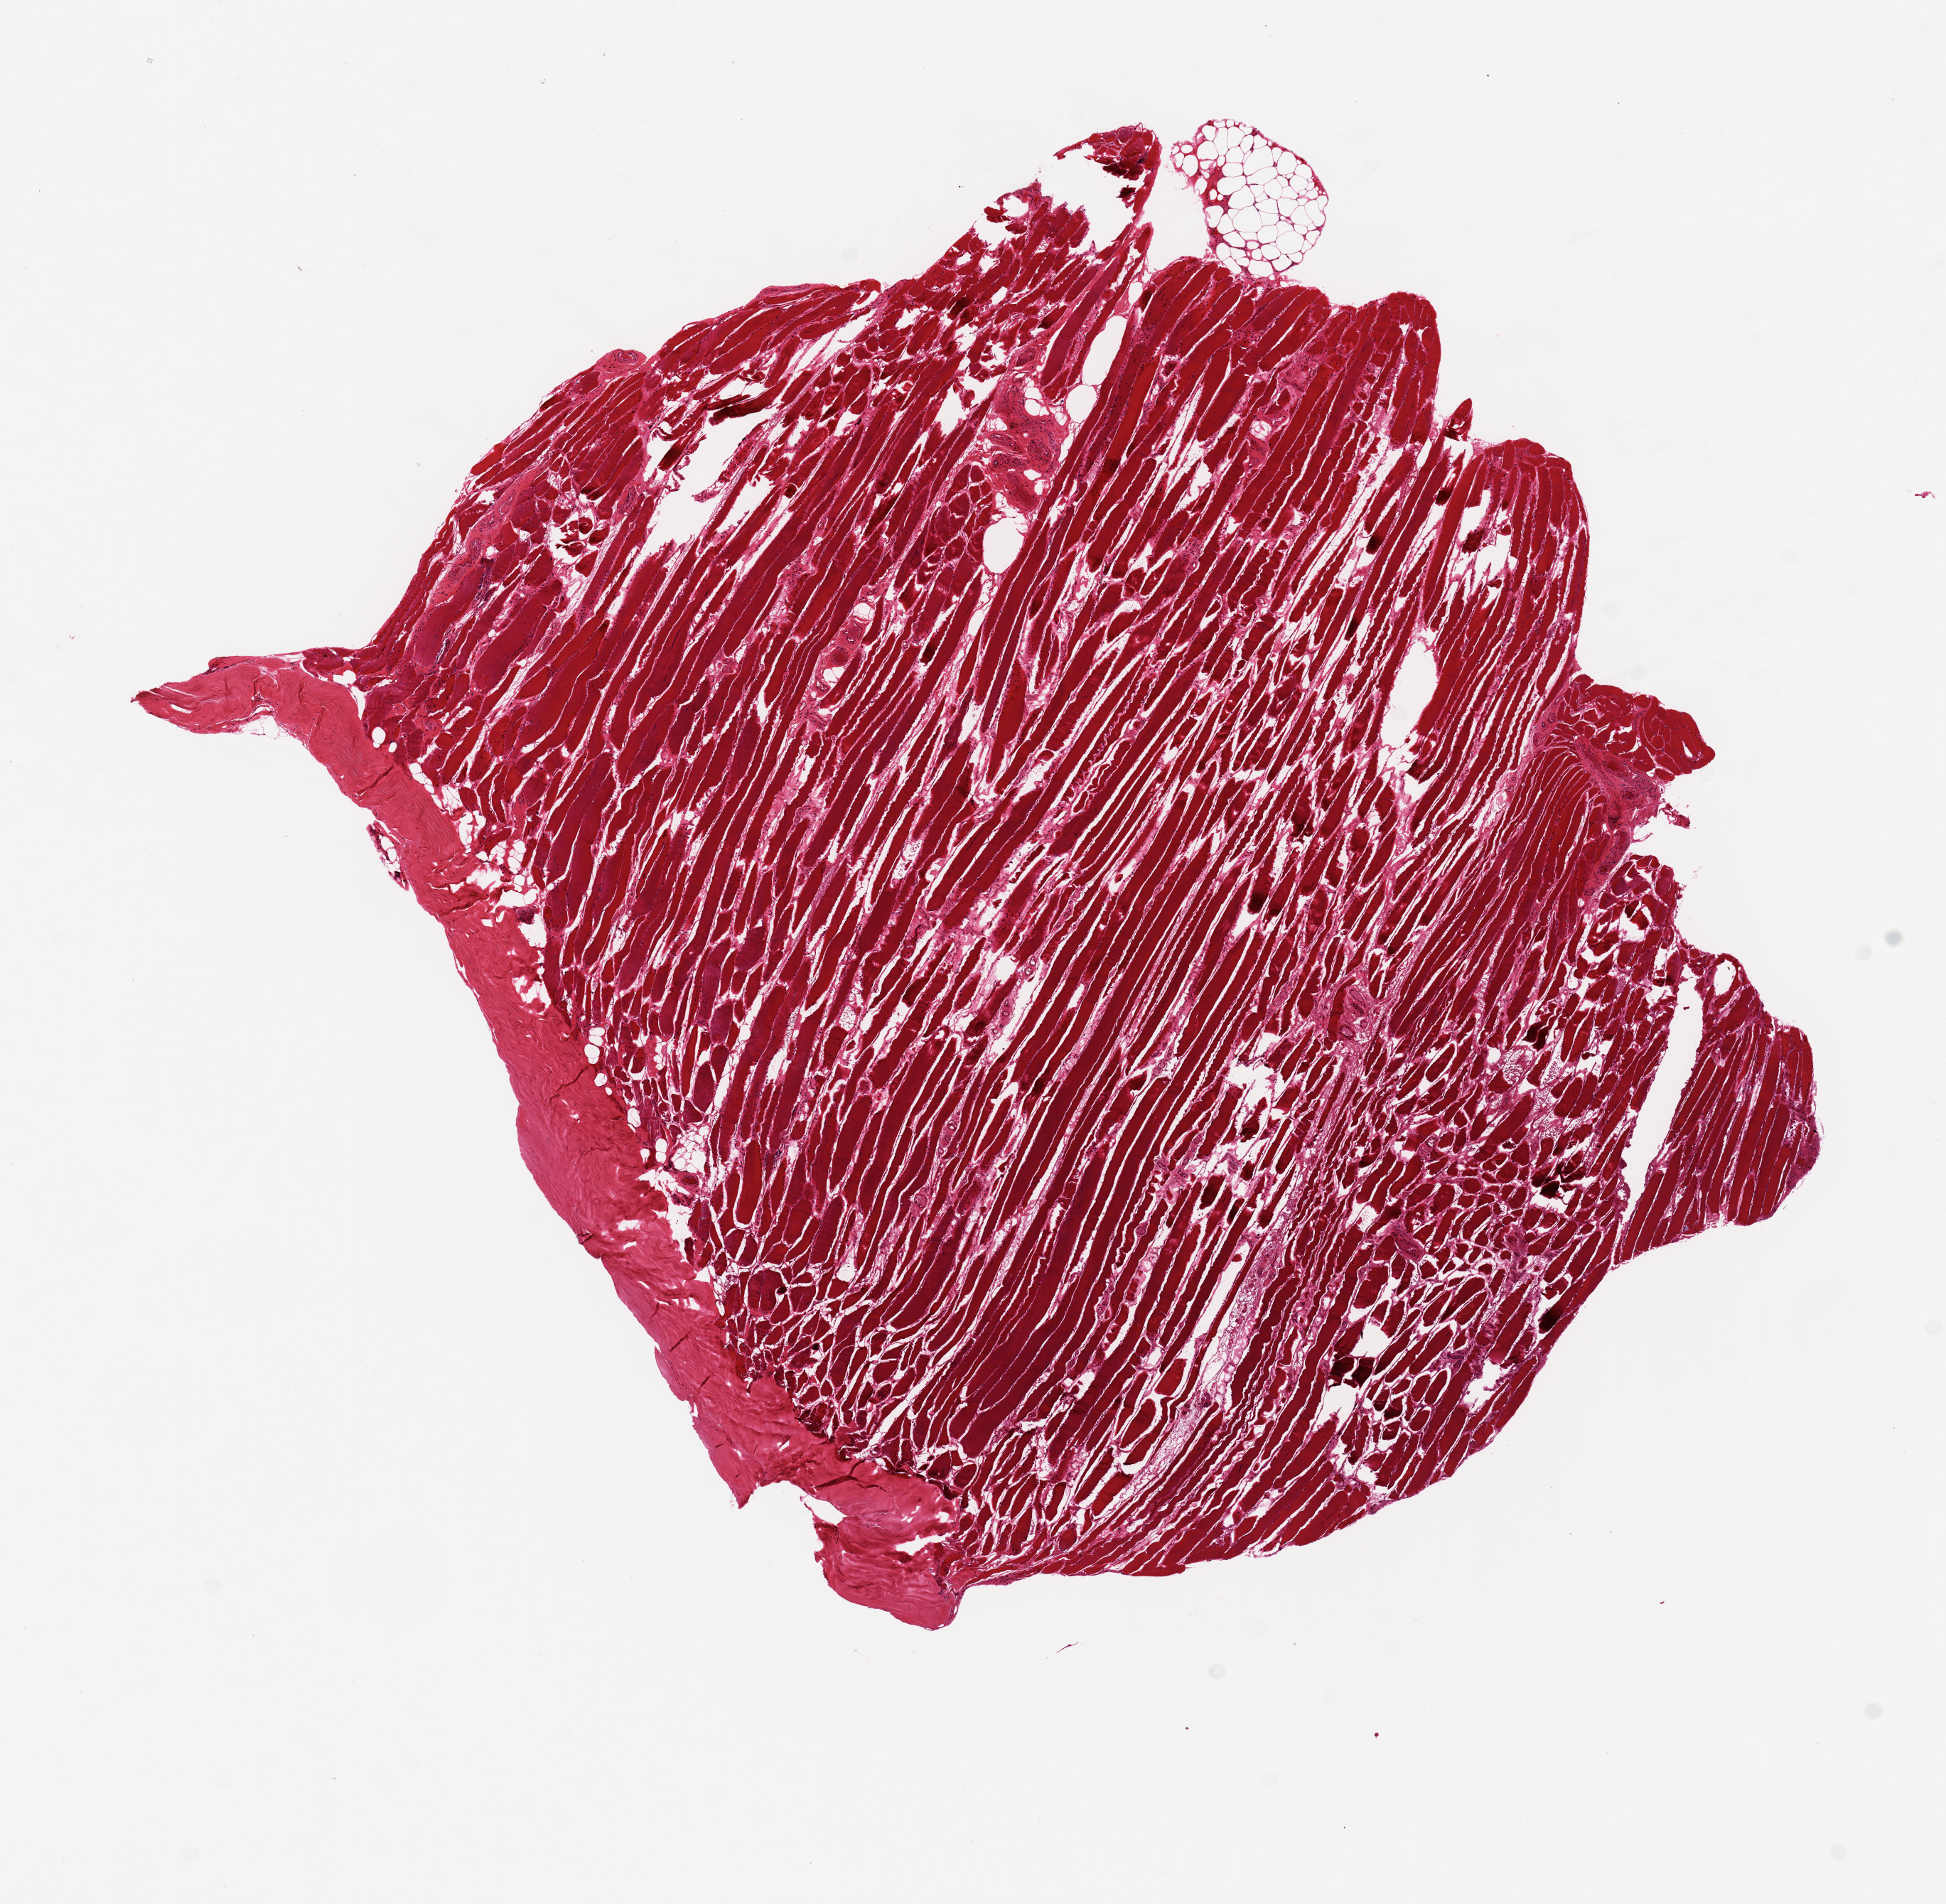
Hematoxylin and eosin (H&E) whole-slide image, whole scanned area (about 10.8 x 10.6 mm, from a 20x scan) shown as a low-resolution overview, PAXgene-fixed, paraffin-embedded tissue, section of skeletal muscle (target tissue), donor tissue sample. Donor sex: male.
Pathologist's review note for this sample: 7x7 mm; 5% fascia.